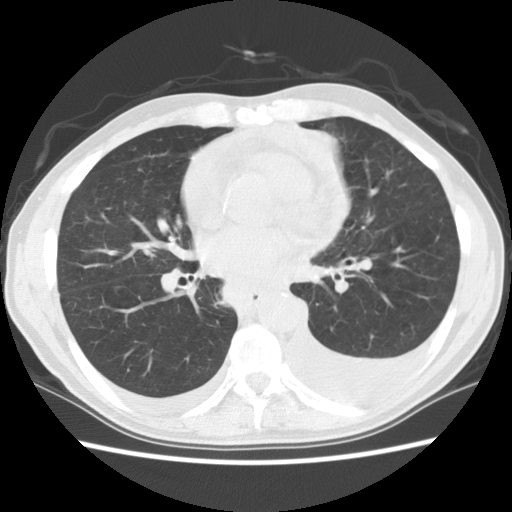
Axial slice from a low-dose chest CT screening exam. First (baseline) screen. Lung window (W 1500 / L -600 HU). Standard (soft-tissue) reconstruction kernel (STANDARD). 140 kVp. Slice 64 of 135 in the series. 512 × 512 image matrix, field of view 346 × 346 mm. Male participant, aged 60 years at enrolment. Current smoker at enrolment.
Expert-annotated lung lesion, box from (x=173, y=241) to (x=308, y=335) px. No non-calcified nodule or mass ≥4 mm was recorded by the screening reader at this exam. Official screen result: negative screen, significant abnormalities not suspicious for lung cancer. Later outcome: lung cancer diagnosed 12 days after this screen — squamous cell carcinoma, NOS, carina, poorly differentiated (G3), stage IV (AJCC 6th edition).